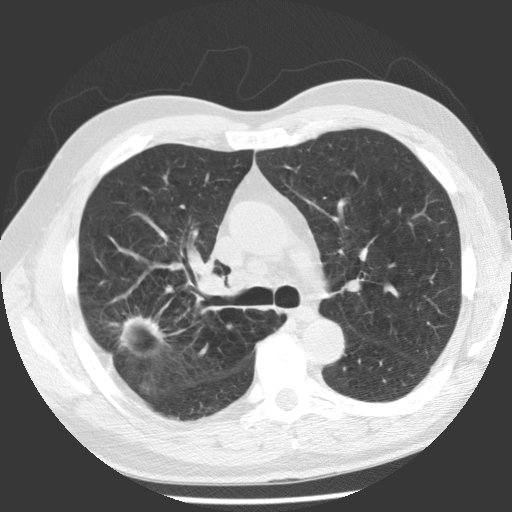
Low-dose screening chest CT, one axial slice; slice 72 of 112 in the series (ordered by position); 140 kVp; lung window (W 1500 / L -600 HU); 2.5 mm slice thickness; 512 × 512 image matrix, field of view 344 × 344 mm.
Structures marked on this image (outlined manually by an expert reader):
- lesion 1 (tumor, upper lobe of right lung): bounding box (x1, y1, x2, y2) in pixels: (119, 315, 164, 349)